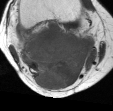
MRI of an extremity soft-tissue mass, one axial slice; position 22 of 45 along the scan axis; MR volume resampled by the dataset authors to the PET/CT grid (not the native acquisition matrix); 113 × 111 image matrix. Female patient. From the clinical record (not read from this slice): histological type: liposarcoma; site of the primary tumour: right thigh.
Outlined on this slice (expert contour drawn on MRI and transferred to this co-registered scan by the dataset authors):
- gross tumour volume (mass): bounding box <19,21,96,89> (left, top, right, bottom; pixels)